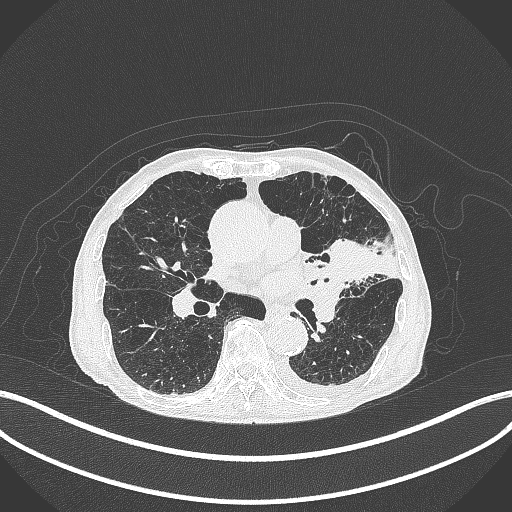
Chest CT, one axial slice. Slice 199 of 385 in the series (ordered by position). 120 kVp. Lung window (W 1500 / L -600 HU). 512 × 512 image matrix. Patient: male, 90 years or older. From the clinical record (not read from this slice): clinical TNM (as recorded): T2b N1 M0.
Annotated regions visible in this slice (bounding box drawn by a radiologist):
- lung tumour (recorded histology: squamous cell carcinoma): bounding box <322,239,378,291> (left, top, right, bottom; pixels)